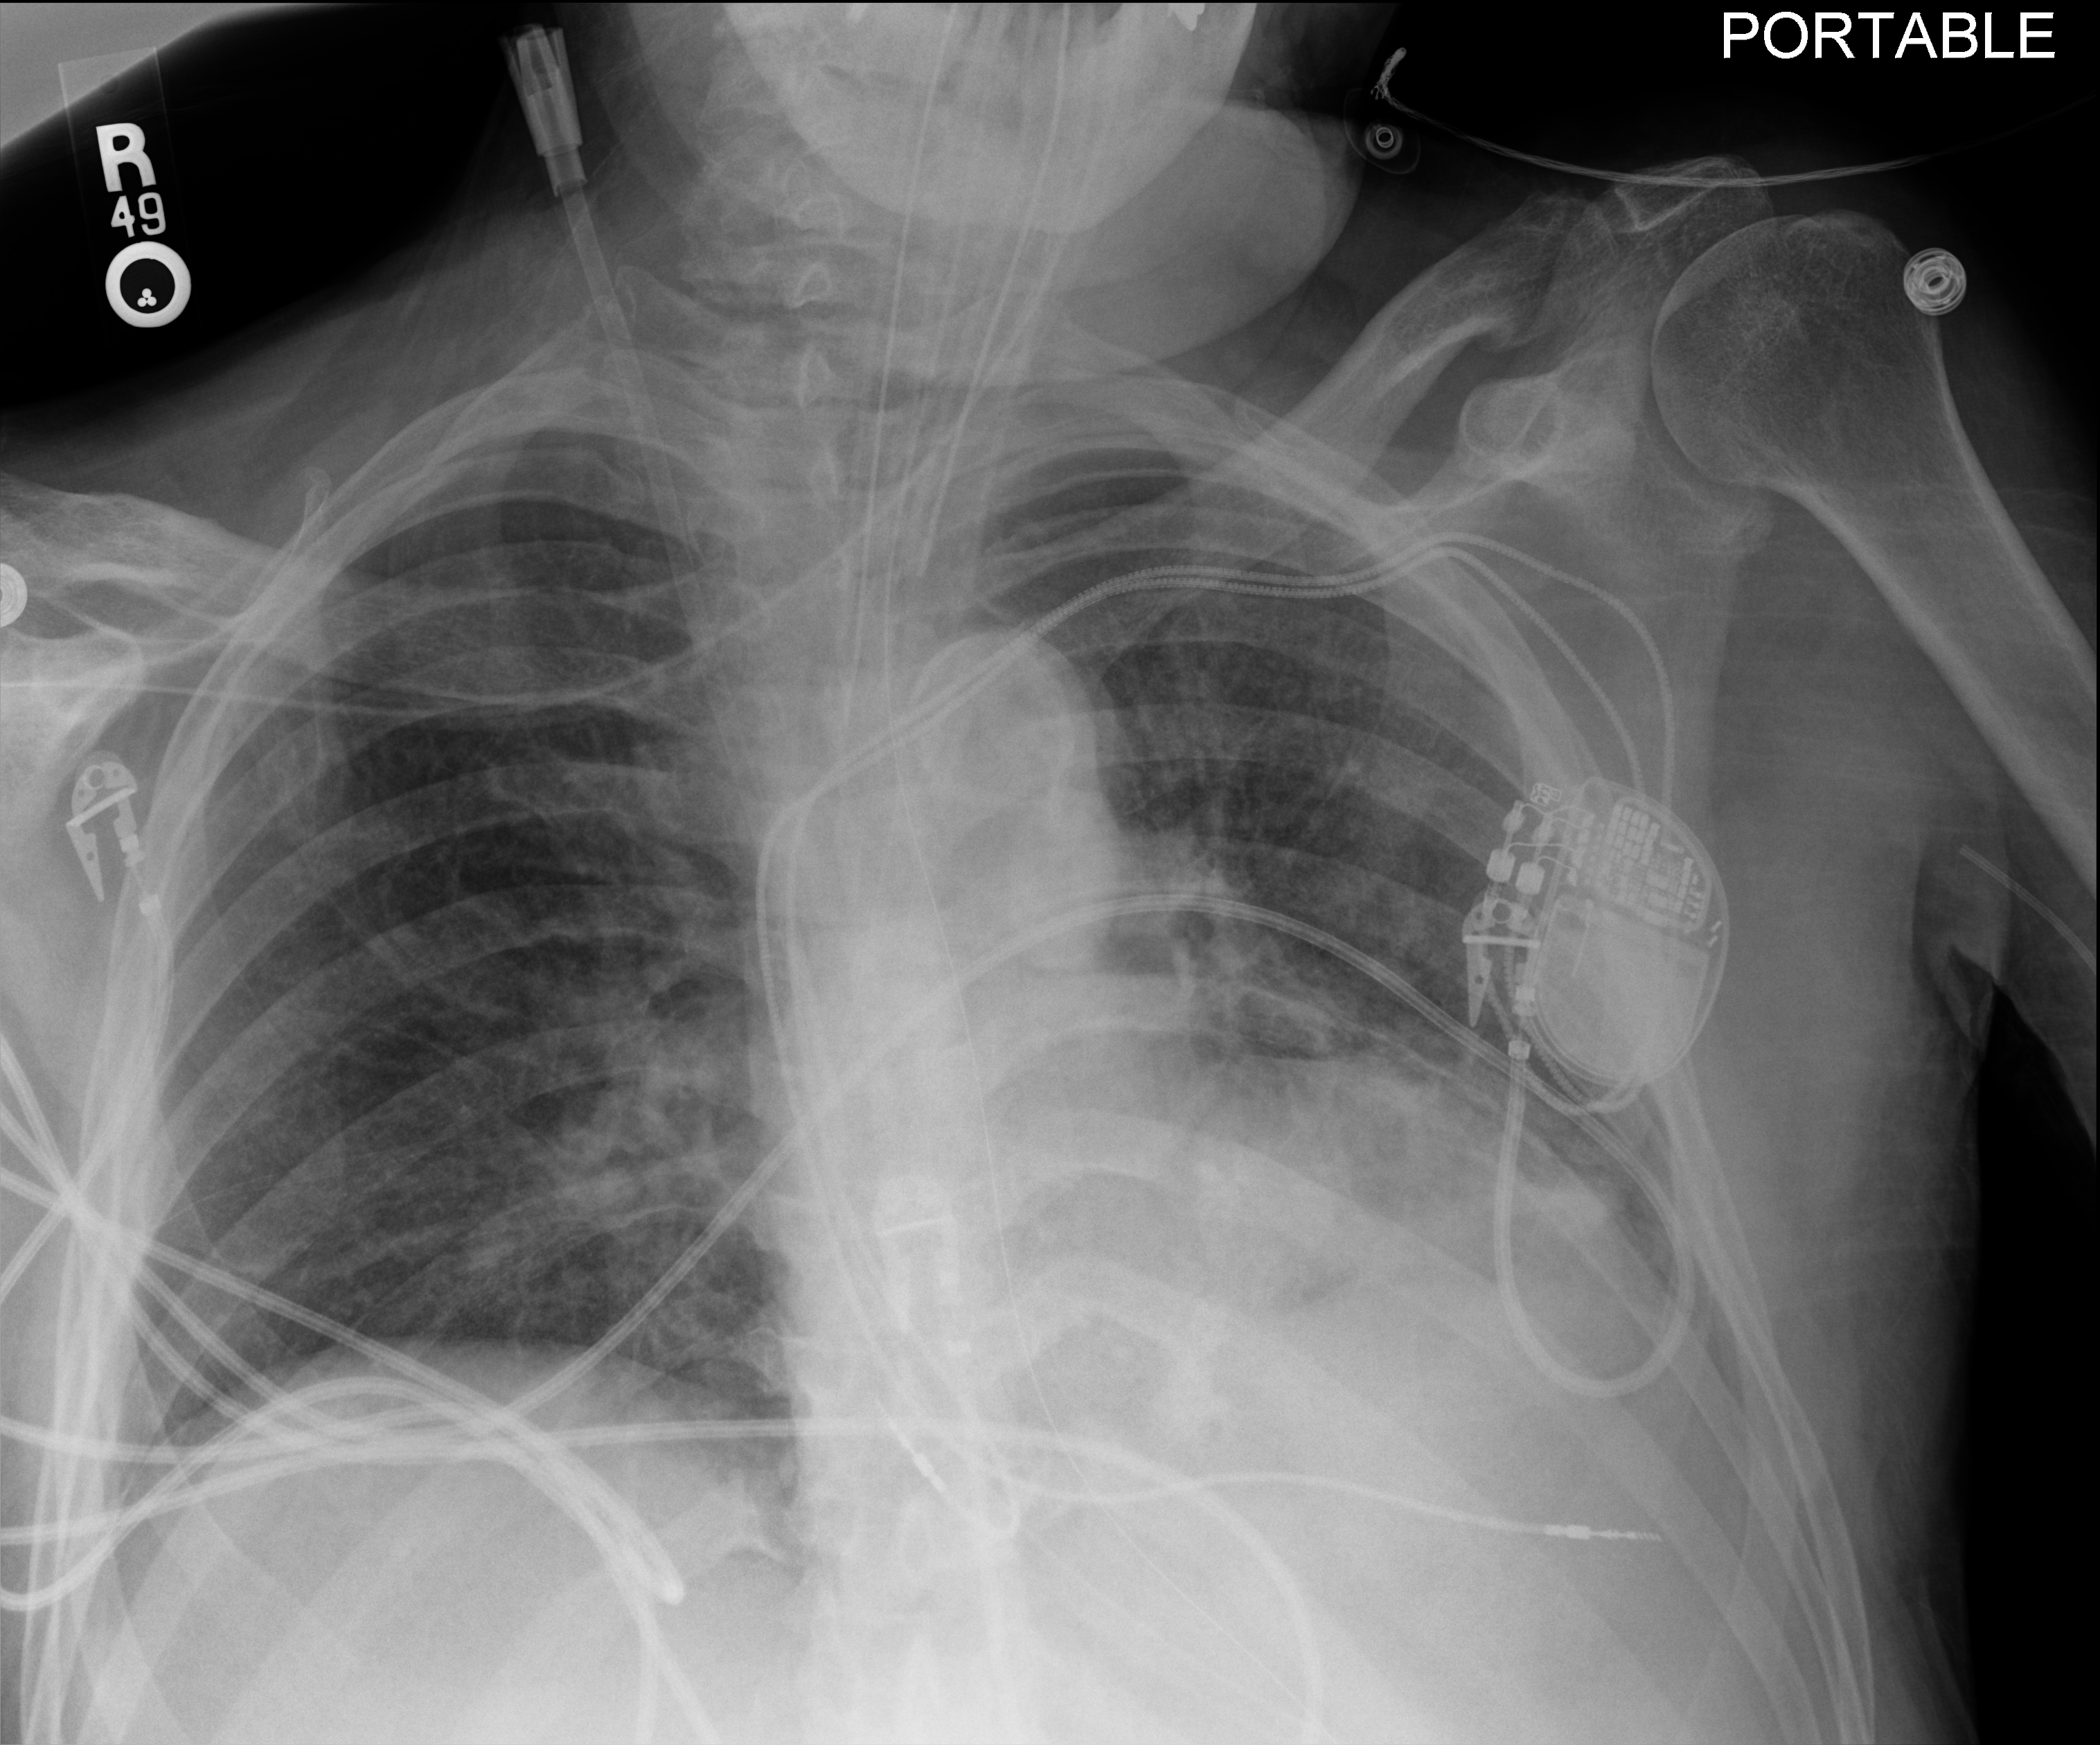
Portable chest radiograph; anteroposterior (AP) projection. Patient hospitalised with COVID-19; male, aged 60–74 years.
Admission-level facts for this patient (not findings on this image; timing relative to this image not recorded): length of hospital stay: 41 days; mechanically ventilated during this hospital stay: yes; admitted to intensive care during this hospital stay: yes.